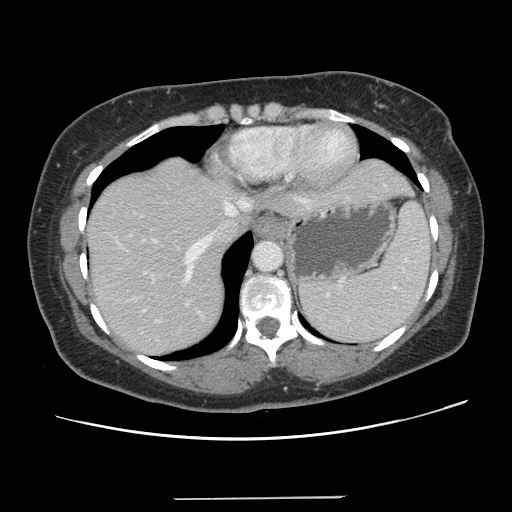
Contrast-enhanced abdominal CT, one axial slice; position 111 of 141 along the scan axis; 120 kVp; intravenous contrast given; soft-tissue window (W 400 / L 40 HU); 2.5 mm slice thickness; 512 × 512 image matrix, field of view 366 × 366 mm. Female patient, age 53 years. From the clinical record (not read from this slice): diagnosis: colorectal cancer liver metastases, imaged before liver resection; multiple liver metastases: no; largest metastasis: 14.5 cm; disease in both lobes: yes.
Structures marked on this image (expert manual segmentation):
- hepatic veins: bounding box (x1, y1, x2, y2) in pixels: (113, 196, 313, 280)
- liver: (87, 158, 410, 356)
- planned liver remnant (the part of the liver to remain after resection): (86, 208, 252, 356)
- portal vein (with intrahepatic branches): (143, 238, 190, 322)